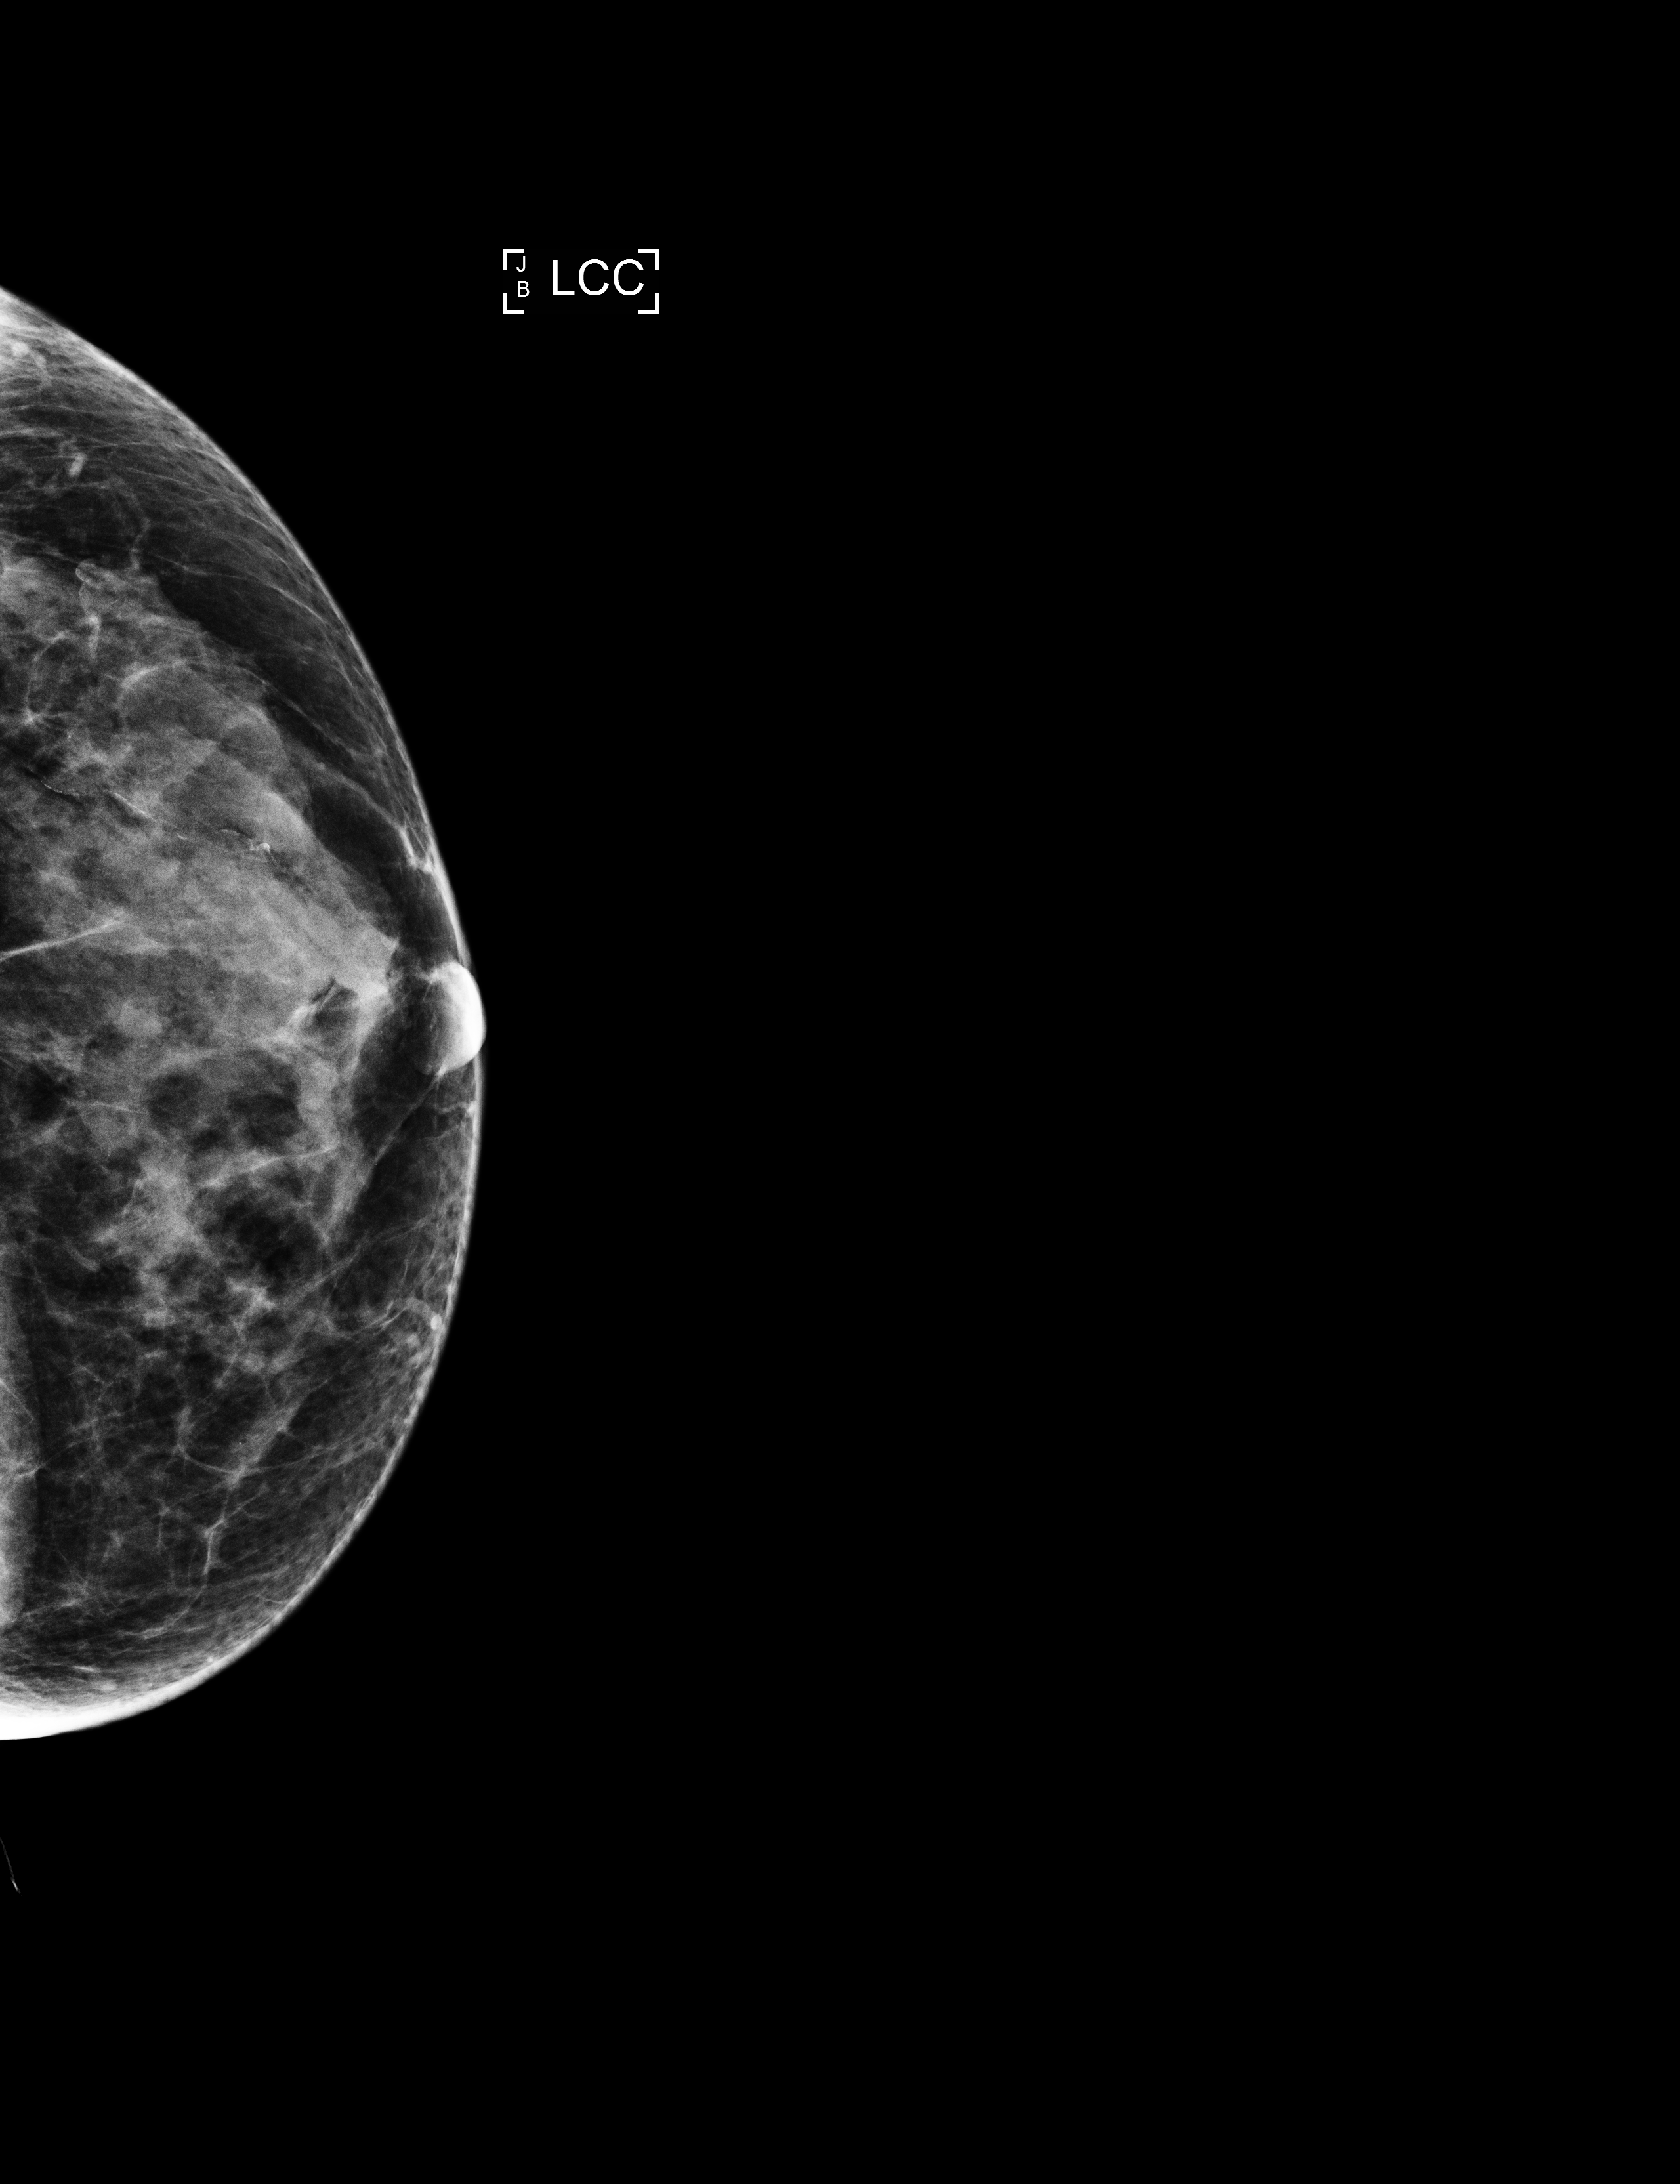
Digital mammogram (FFDM); left breast; craniocaudal (CC) view; screening examination; compressed breast thickness 38 mm; system: Selenia Dimensions. Patient: female, 58 years.
Breast density at the screening exam (both breasts): heterogeneously dense (BI-RADS density category c). Final BI-RADS category for the screening round (tomosynthesis exam, both breasts): category 1. Recall: no recall after this screen.